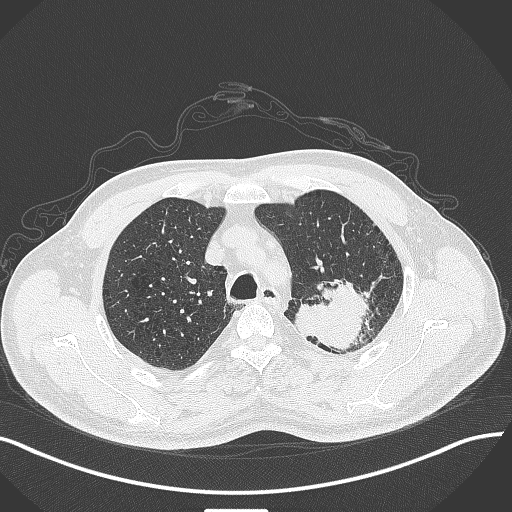
Chest CT, one axial slice; position 332 of 429 along the scan axis; reconstruction kernel B70f; 120 kVp; lung window (W 1500 / L -600 HU); 1 mm slice thickness; 512 × 512 image matrix, field of view 400 × 400 mm. Male patient, age 55 years. Case-level facts recorded for this patient, not image findings: clinical TNM (as recorded): T3 N0 M1c.
Outlined on this slice (bounding box drawn by a radiologist):
- lung tumour (recorded histology: adenocarcinoma): box from (x=296, y=278) to (x=378, y=353) px